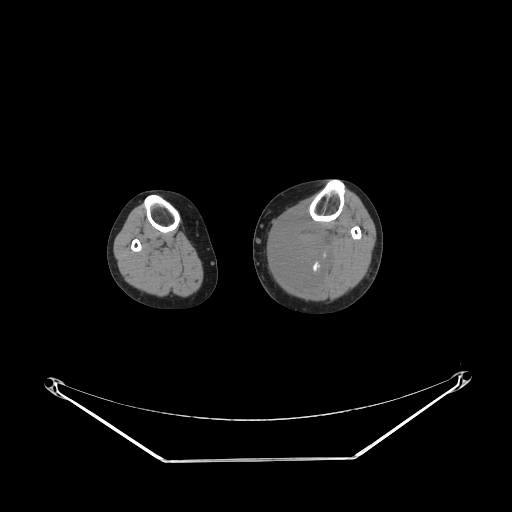
CT of an extremity soft-tissue mass (from a PET/CT study), one axial slice. Slice 148 of 223 in the series (ordered by position). Reconstruction kernel STANDARD. 140 kVp. Soft-tissue window (W 400 / L 40 HU). 512 × 512 image matrix, field of view 500 × 500 mm. Female patient. From the clinical record (not read from this slice): histological type: extraskeletal high grade osteogenic sarcoma; grade: high; site of the primary tumour: left calf.
Outlined on this slice (expert contour drawn on MRI and transferred to this co-registered scan by the dataset authors):
- gross tumour volume (mass): box from (x=272, y=217) to (x=334, y=284) px